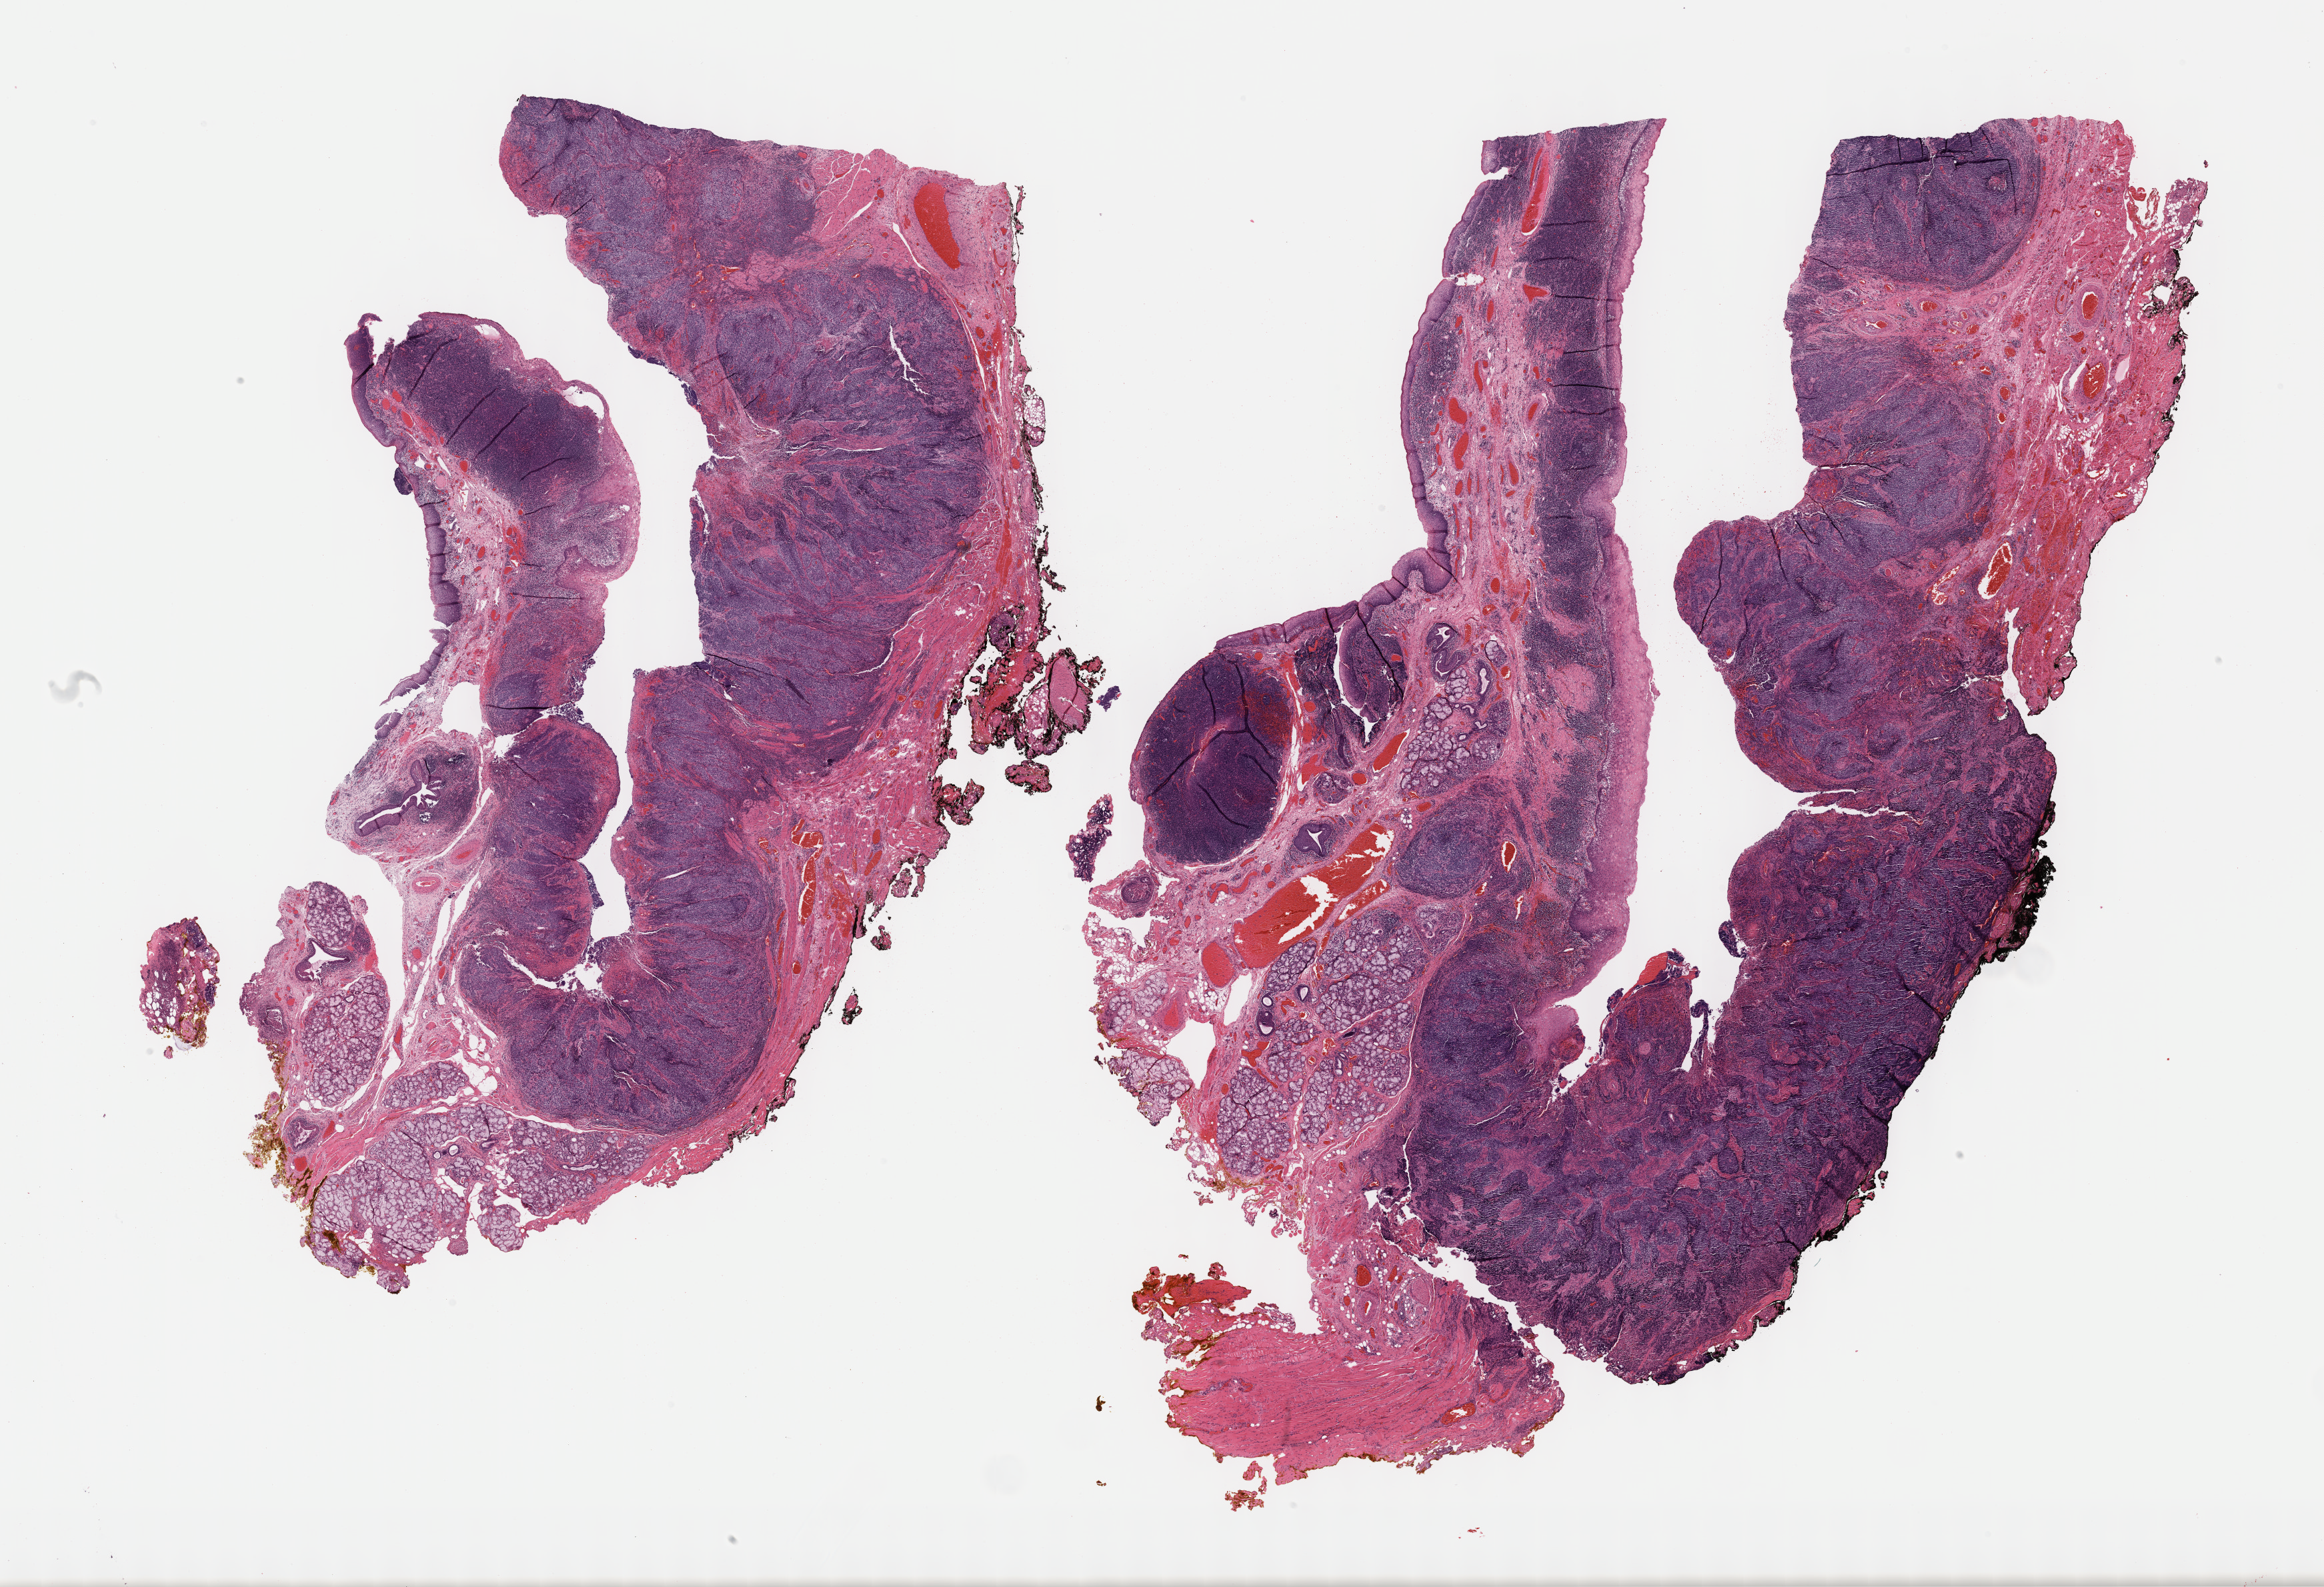
Whole-slide histology image, Hematoxylin and eosin (H&E) stained — shown as a low-resolution overview of the whole scanned area (about 28.2 x 19.3 mm). Formalin-fixed paraffin-embedded (FFPE) diagnostic section. Head and neck, primary tumour sample. Patient: male, age at initial diagnosis 56 years. Histologic grade: G3 (poorly differentiated).
TNM: T2 N2b M0. AJCC pathologic stage: IVA (7th edition). Histologic diagnosis: Squamous cell carcinoma, large cell, nonkeratinizing, NOS (tonsil, NOS). Laterality: right.